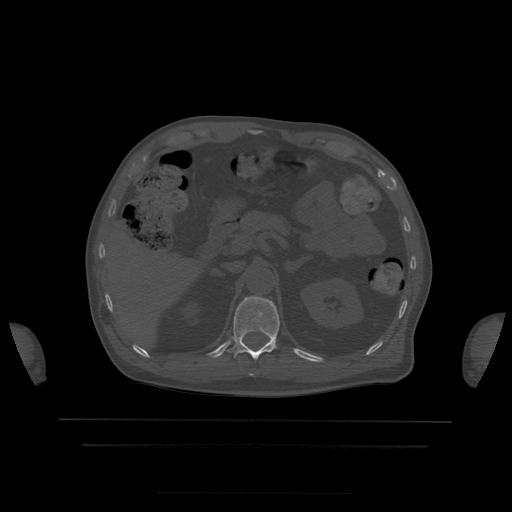
CT including the spine, one axial slice; position 195 of 522 along the scan axis; bone window (W 1800 / L 400 HU); 512 × 512 image matrix, field of view 436 × 436 mm. Patient age 68 years. Case-level facts recorded for this patient, not image findings: primary cancer: urothelial.
Structures marked on this image (semi-automatic segmentation, software-assisted and operator-edited):
- T11 vertebra: bounding box <250,374,253,376> (left, top, right, bottom; pixels)
- T12 vertebra: <229,296,280,360>